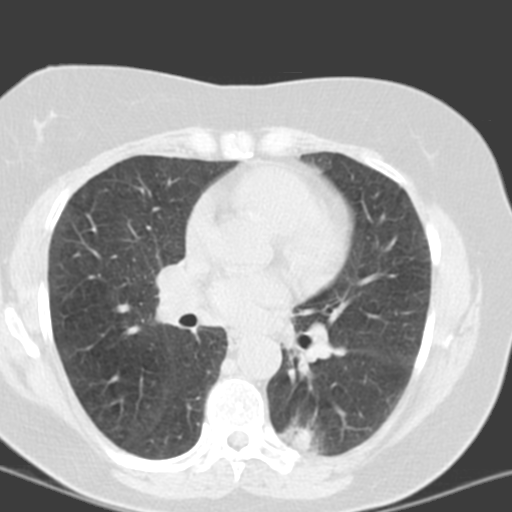
Axial slice from a low-dose chest CT screening exam. Third screening round (two years after baseline). Lung window (W 1500 / L -600 HU). Standard (soft-tissue) reconstruction kernel (B). Female participant, aged 55 years at enrolment. Current smoker at enrolment.
Expert-annotated lung lesion, bounding box (x1, y1, x2, y2) in pixels: (283, 408, 363, 462). The screening reader recorded 6 non-calcified nodules or masses ≥4 mm on this exam; which of them this box marks is not recorded. Official screen result: positive, no significant change: stable abnormalities potentially related to lung cancer, unchanged since the prior screening exam. Later outcome: lung cancer diagnosed 357 days after this screen — adenocarcinoma with mixed subtypes, left lower lobe, poorly differentiated (G3), stage IA (AJCC 6th edition), 21 mm at pathology.